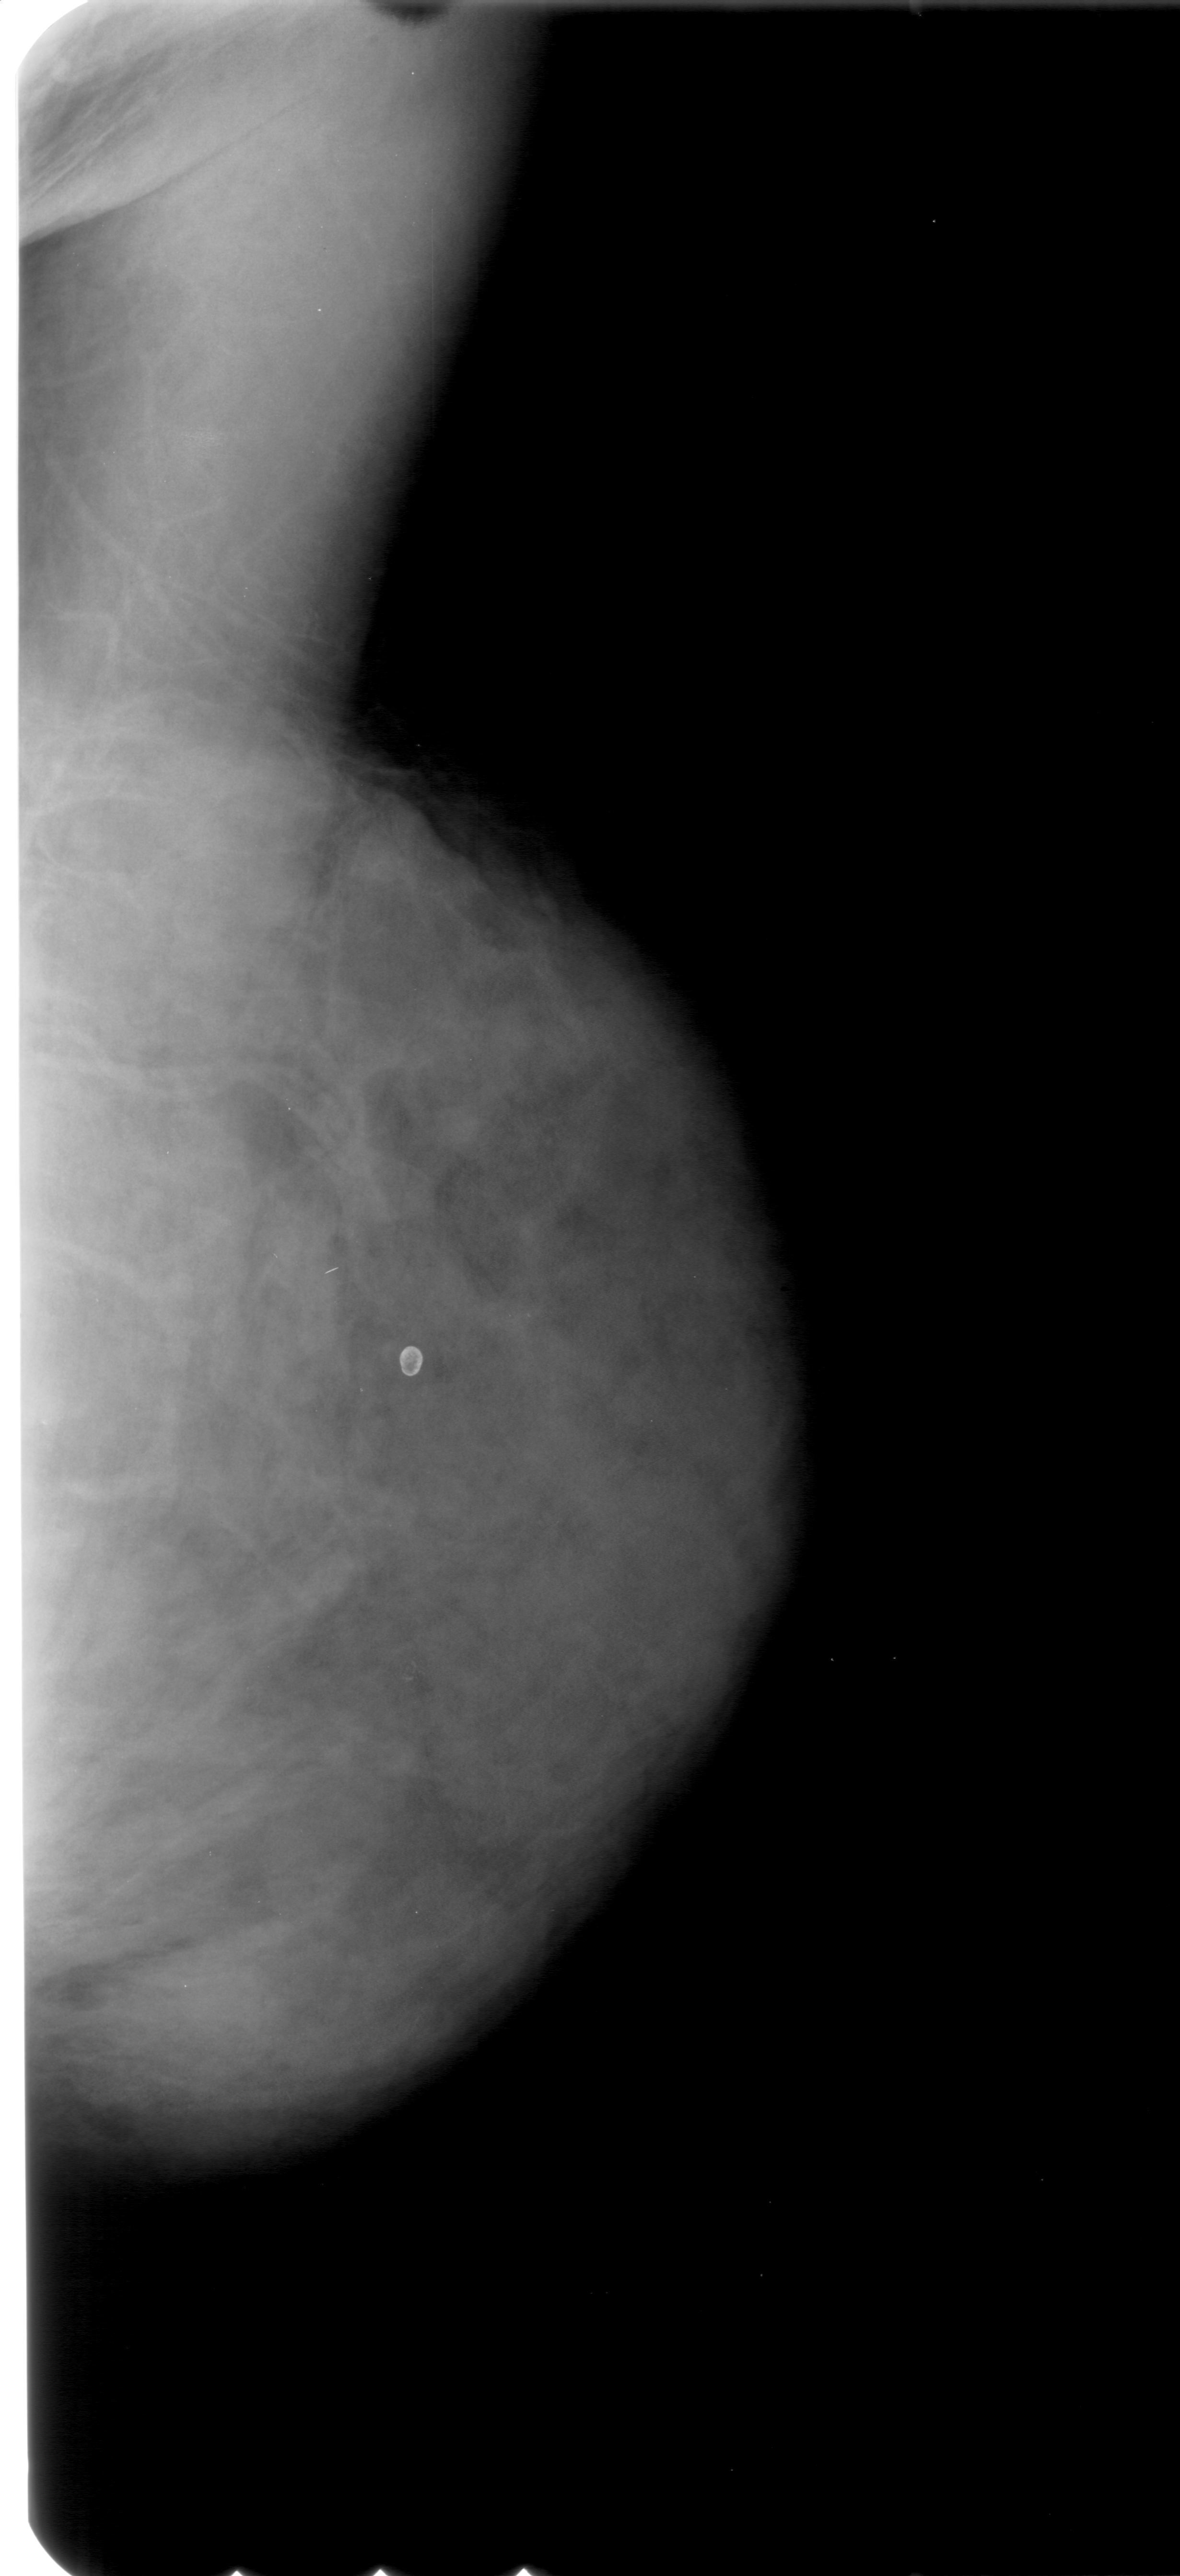
Mammogram (digitized film); right breast; MLO view; breast composition: extremely dense (BI-RADS density category 4 of 4).
Abnormality record for this image: calcifications, morphology pleomorphic, distribution clustered; BI-RADS assessment category 3; subtlety rating 1 on a 1 (subtle) to 5 (obvious) scale; pathology result (as recorded, not read from the image): benign.